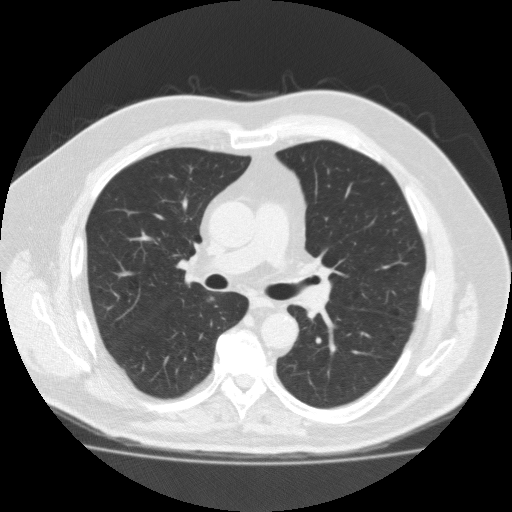
Low-dose screening chest CT, one axial slice. Slice 114 of 183 in the series (ordered by position). 120 kVp. Lung window (W 1500 / L -600 HU). 2 mm slice thickness. 512 × 512 image matrix.
Annotated regions visible in this slice (manually delineated by an expert):
- lesion 1 (tumor, lower lobe of right lung): bounding box [x1, y1, x2, y2] px = [210, 297, 214, 300]